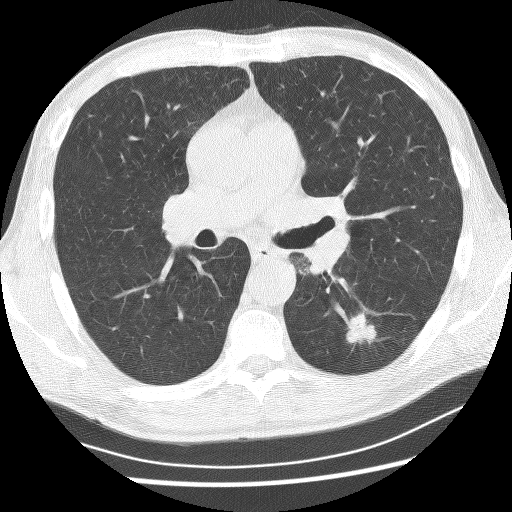
Chest CT (low-dose screening protocol), one axial image, baseline annual screen, lung window (W 1500 / L -600 HU), 2.5 mm slice thickness, lung (sharp) reconstruction kernel (BONE), slice 111 of 253 in the series. Male, age 62 years at enrolment.
• Expert reader's lesion annotation, bounding box [x1, y1, x2, y2] px = [329, 306, 383, 351].
• Reader record for this screening exam (exam-level; its link to the box is not recorded): non-calcified nodule or mass ≥4 mm, left lower lobe, 21 × 17 mm, spiculated (stellate) margins, soft tissue attenuation.
• Official screen result: positive, change unspecified: nodule(s) >= 4 mm or enlarging nodule(s), mass(es), or other non-specific abnormalities suspicious for lung cancer.
• Later outcome: lung cancer diagnosed 58 days after this screen — non-small cell carcinoma, left lower lobe, poorly differentiated (G3), stage IA (AJCC 6th edition), 11 mm at pathology.